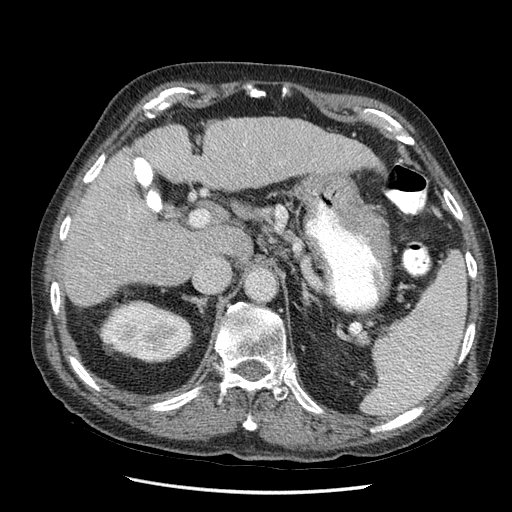
Contrast-enhanced abdominal CT (liver protocol), one axial slice. 120 kVp. Soft-tissue window (W 400 / L 40 HU). 512 × 512 image matrix, field of view 360 × 360 mm. From the clinical record (not read from this slice): diagnosis: hepatocellular carcinoma (patient treated with transarterial chemoembolisation; whether this scan precedes or follows treatment is not stated here); TNM stage (as recorded): Stage-I.
Annotated regions visible in this slice (semi-automatically segmented with operator editing):
- liver parenchyma outside the tumour (the mass and vessels are separate outlines, so this box may not span the whole liver): bounding box <60,119,366,310> (left, top, right, bottom; pixels)
- liver vessels: <124,143,243,245>